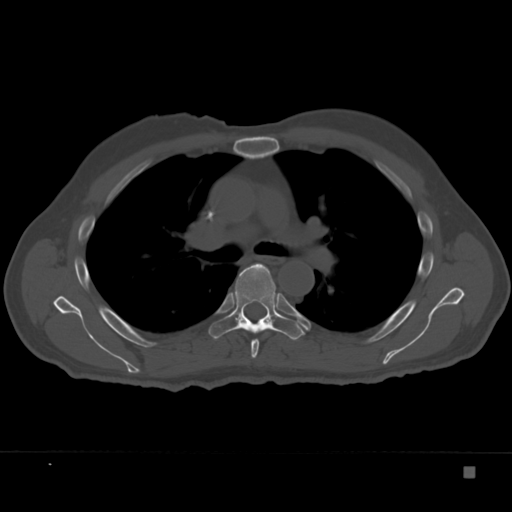
CT including the spine, one axial slice. Position 245 of 332 along the scan axis. 120 kVp. Bone window (W 1800 / L 400 HU). 1.5 mm slice thickness. 512 × 512 image matrix, field of view 389 × 389 mm. Patient: male, 72 years. From the clinical record (not read from this slice): primary cancer: skeletal.
Annotated regions visible in this slice (semi-automatic segmentation, software-assisted and operator-edited):
- T5 vertebra: bounding box [x1, y1, x2, y2] px = [251, 339, 260, 358]
- T6 vertebra: [208, 263, 305, 341]